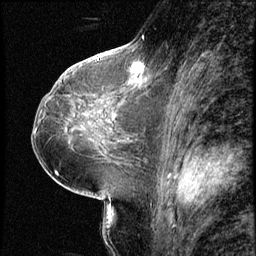
Breast MRI (dynamic contrast-enhanced), one sagittal slice; position 34 of 66 along the scan axis; 3 images stored at this slice position (order not interpretable as contrast timing); 1.5 T; TE 4.2 ms, TR 8.7 ms; 2.5 mm slice thickness; 256 × 256 image matrix. Female patient, age 38 years. From the clinical record (not read from this slice): setting: breast cancer imaged before/during neoadjuvant chemotherapy; receptor status: triple-negative.
Outlined on this slice (semi-automatically segmented with operator editing):
- analysis volume of interest (the breast-tissue region the enhancement analysis was run in; not a lesion): bounding box [x1, y1, x2, y2] px = [128, 57, 149, 78]
- tumour enhancement mask (voxels above the 140 % enhancement threshold inside the analysis volume of interest): [129, 63, 145, 73]